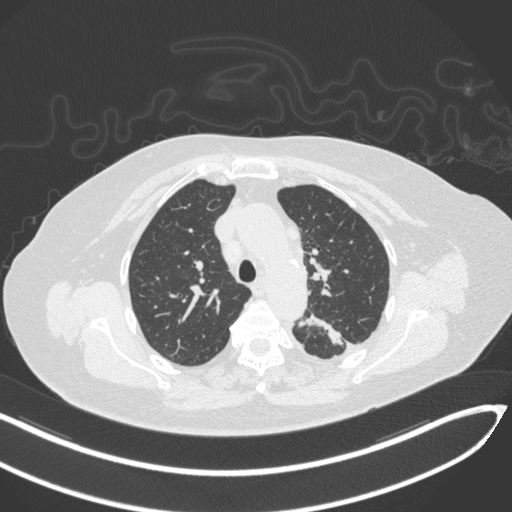
Chest CT, one axial slice. Position 227 of 270 along the scan axis. Reconstruction kernel B31f. 120 kVp. Lung window (W 1500 / L -600 HU). 1 mm slice thickness. 512 × 512 image matrix, field of view 400 × 400 mm. Female patient, age 76 years. Case-level facts recorded for this patient, not image findings: clinical TNM (as recorded): T1c N0 M0.
Outlined on this slice (rectangle marked by the reading radiologist):
- lung tumour (recorded histology: adenocarcinoma): bounding box <296,311,346,353> (left, top, right, bottom; pixels)